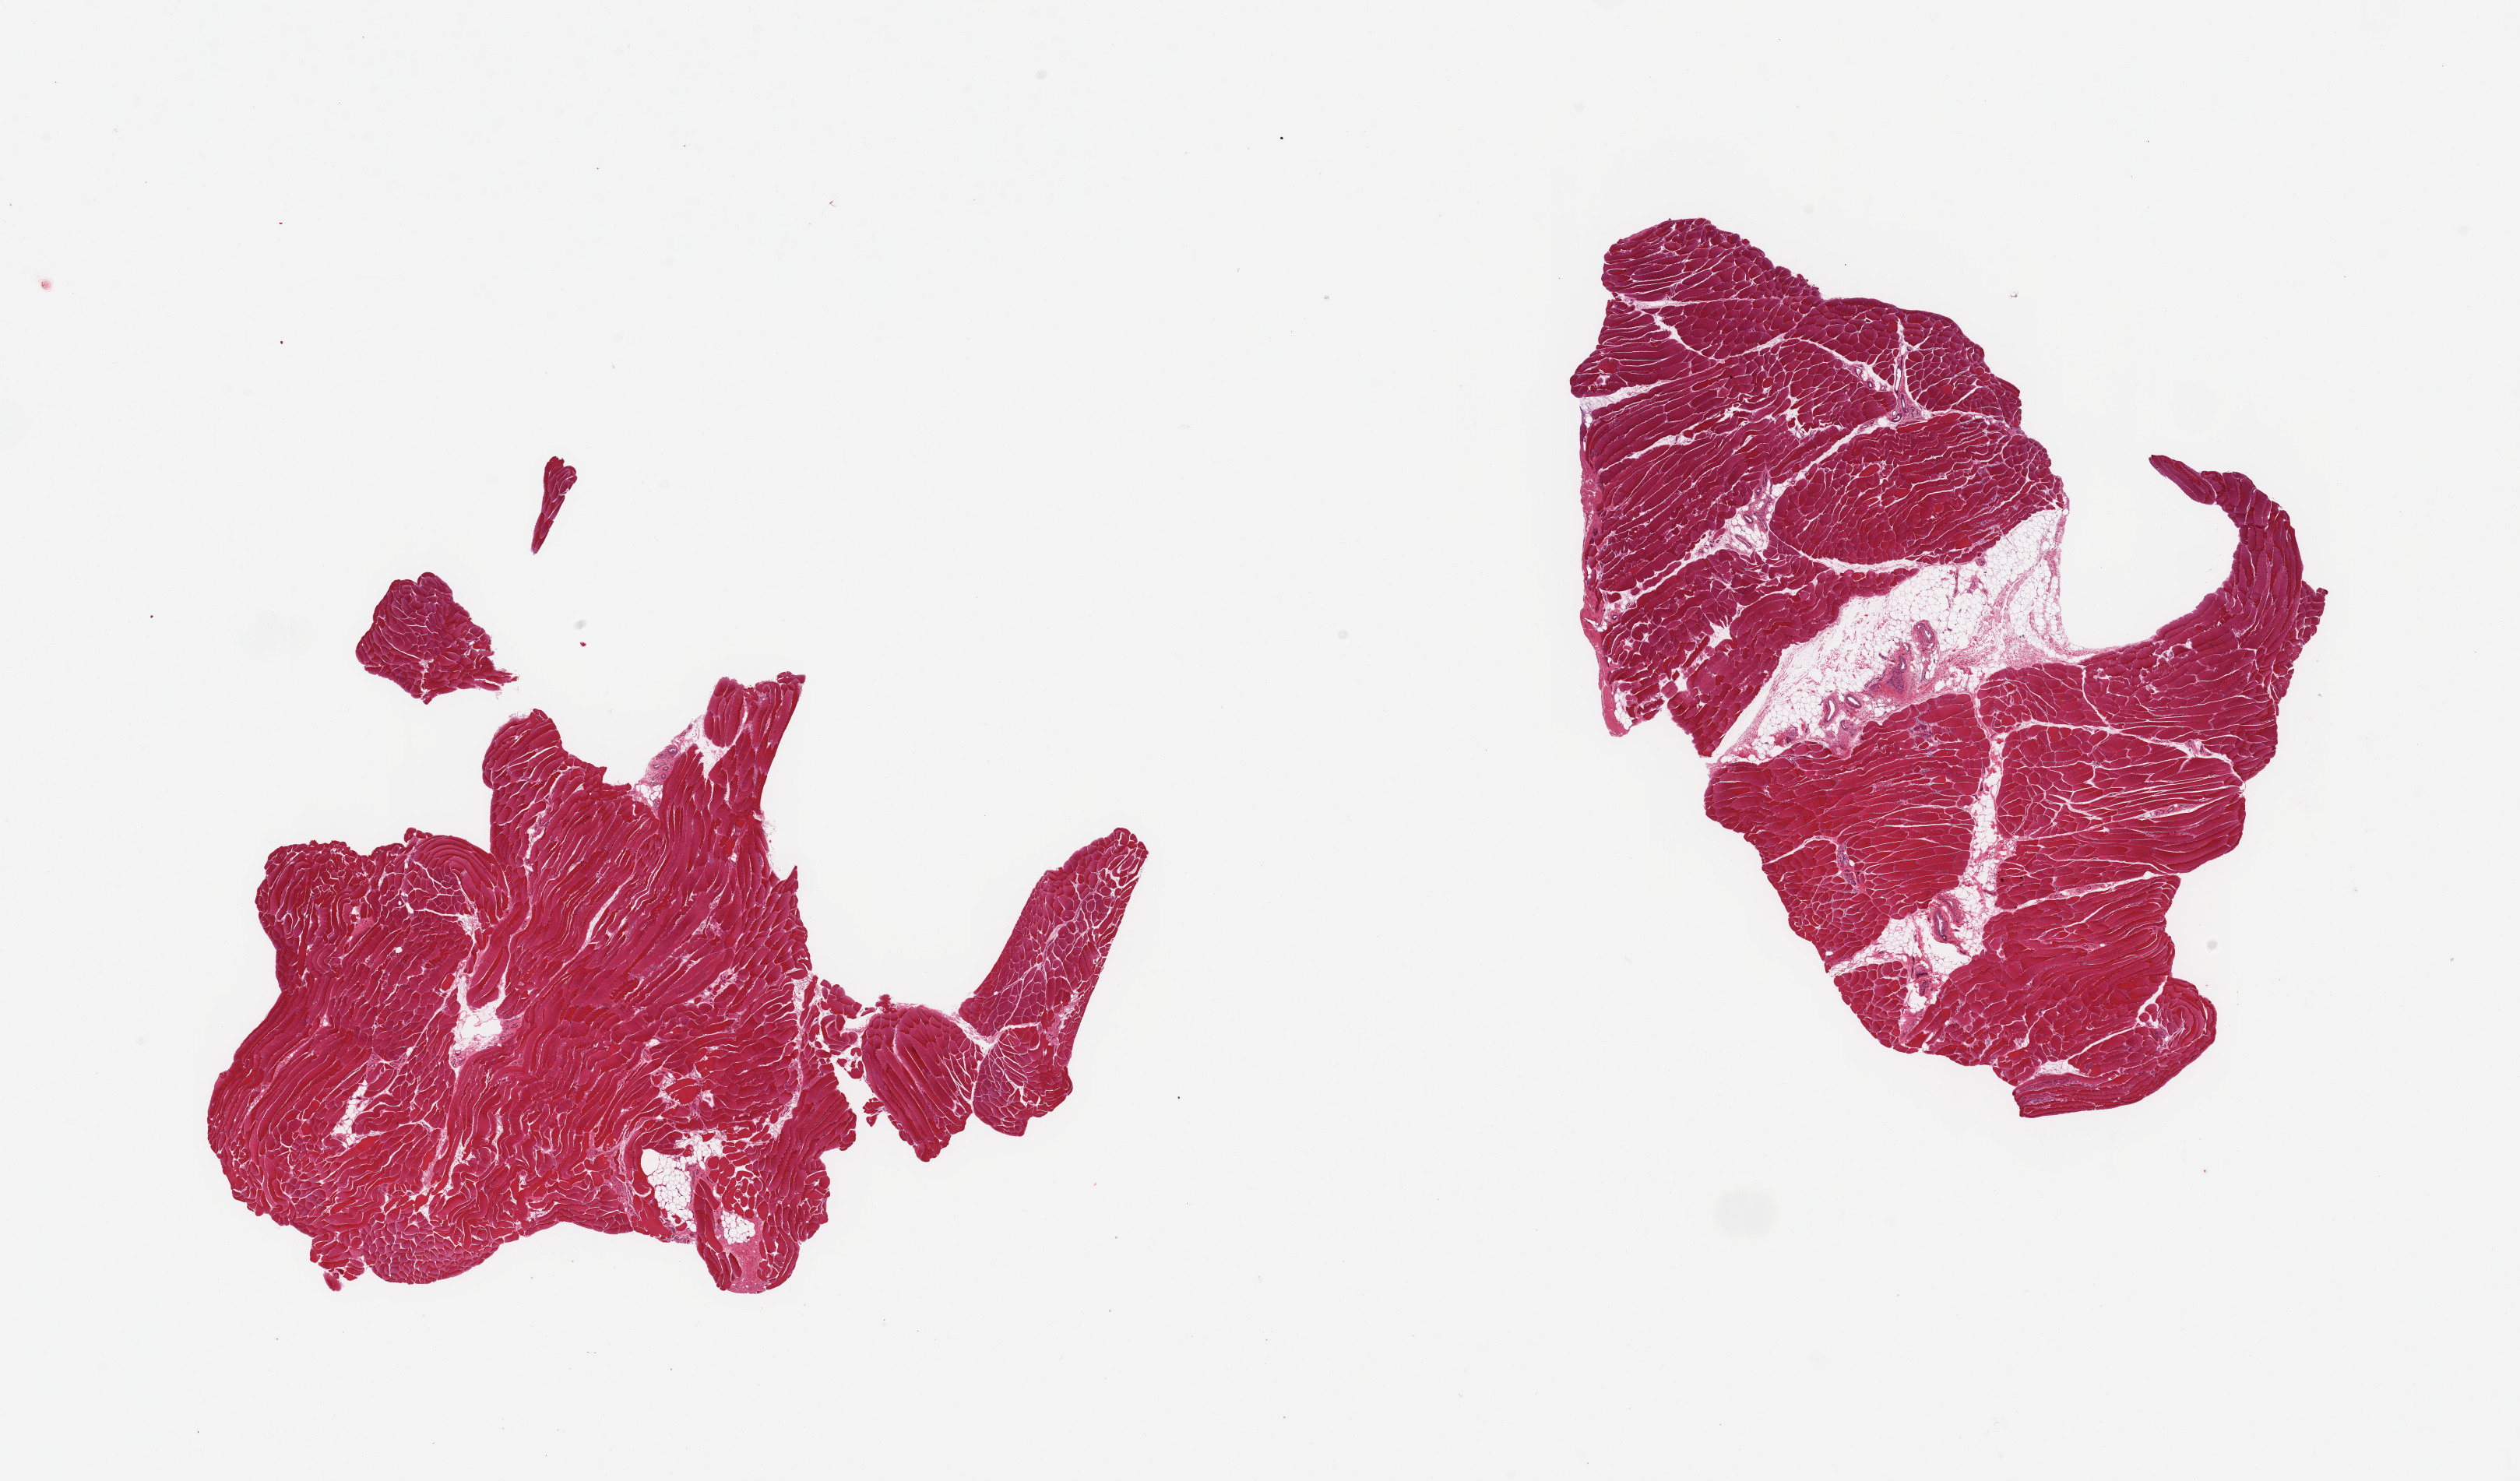
Digitized haematoxylin and eosin-stained section, shown as a low-resolution overview of the whole scanned area (about 25.6 x 15.0 mm). PAXgene-fixed, paraffin-embedded tissue. Sampled site (target tissue): skeletal muscle. Tissue donor sample. Male donor.
• pathologist's review note for this sample: 2 pieces; 5 & 20% internal fat content